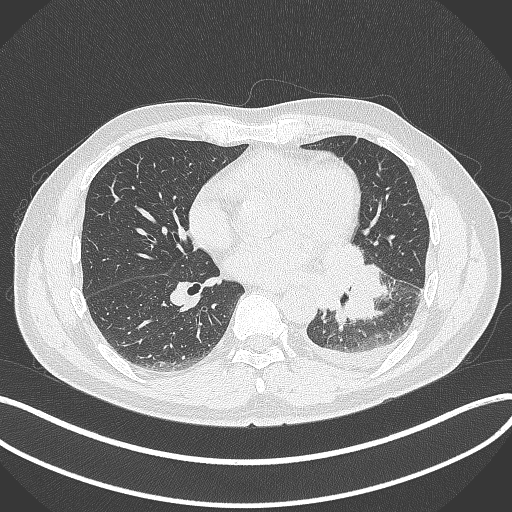
Chest CT, one axial slice. Slice 160 of 342 in the series (ordered by position). Lung window (W 1500 / L -600 HU). 512 × 512 image matrix, field of view 400 × 400 mm. Patient: male, 58 years. Case-level facts recorded for this patient, not image findings: clinical TNM (as recorded): T3 N1 M1b; histopathological grade: G3.
Outlined on this slice (bounding box drawn by a radiologist):
- lung tumour (recorded histology: small cell carcinoma): box from (x=319, y=239) to (x=384, y=328) px